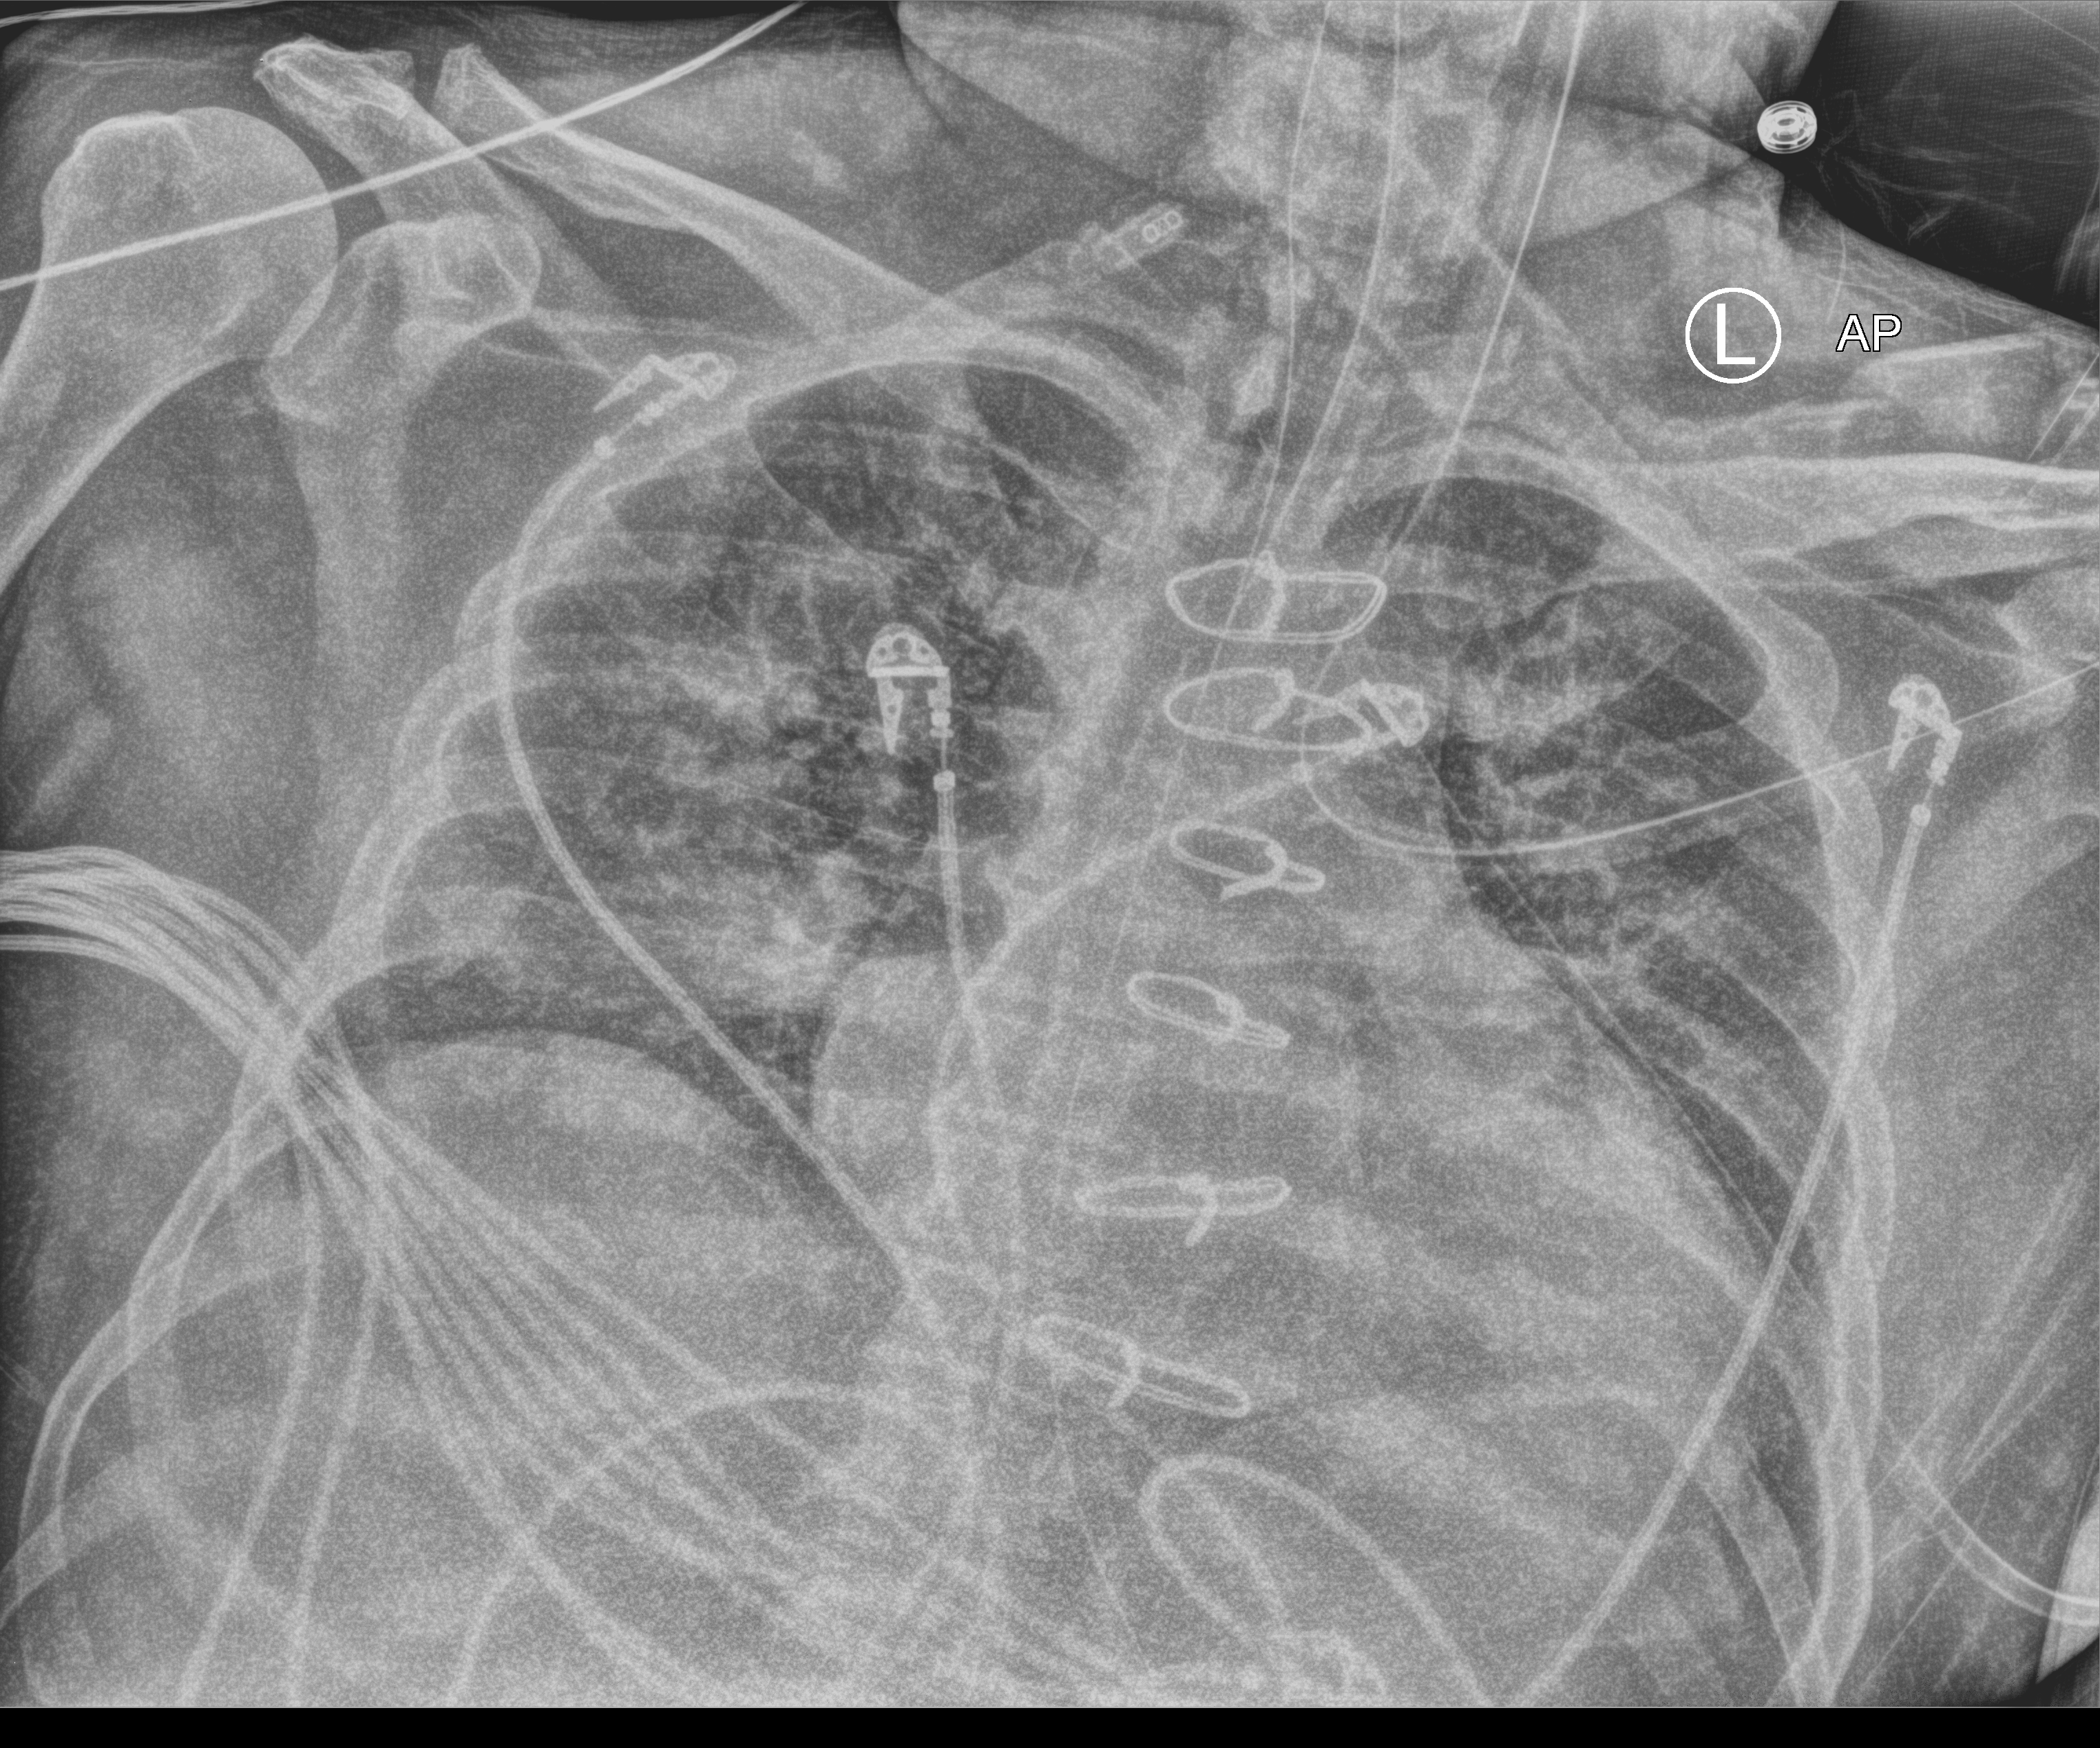
Portable chest radiograph; anteroposterior (AP) projection. Patient hospitalised with COVID-19, aged 18–59 years.
Admission-level facts for this patient (not findings on this image; timing relative to this image not recorded):
- mechanically ventilated during this hospital stay: yes
- admitted to intensive care during this hospital stay: yes